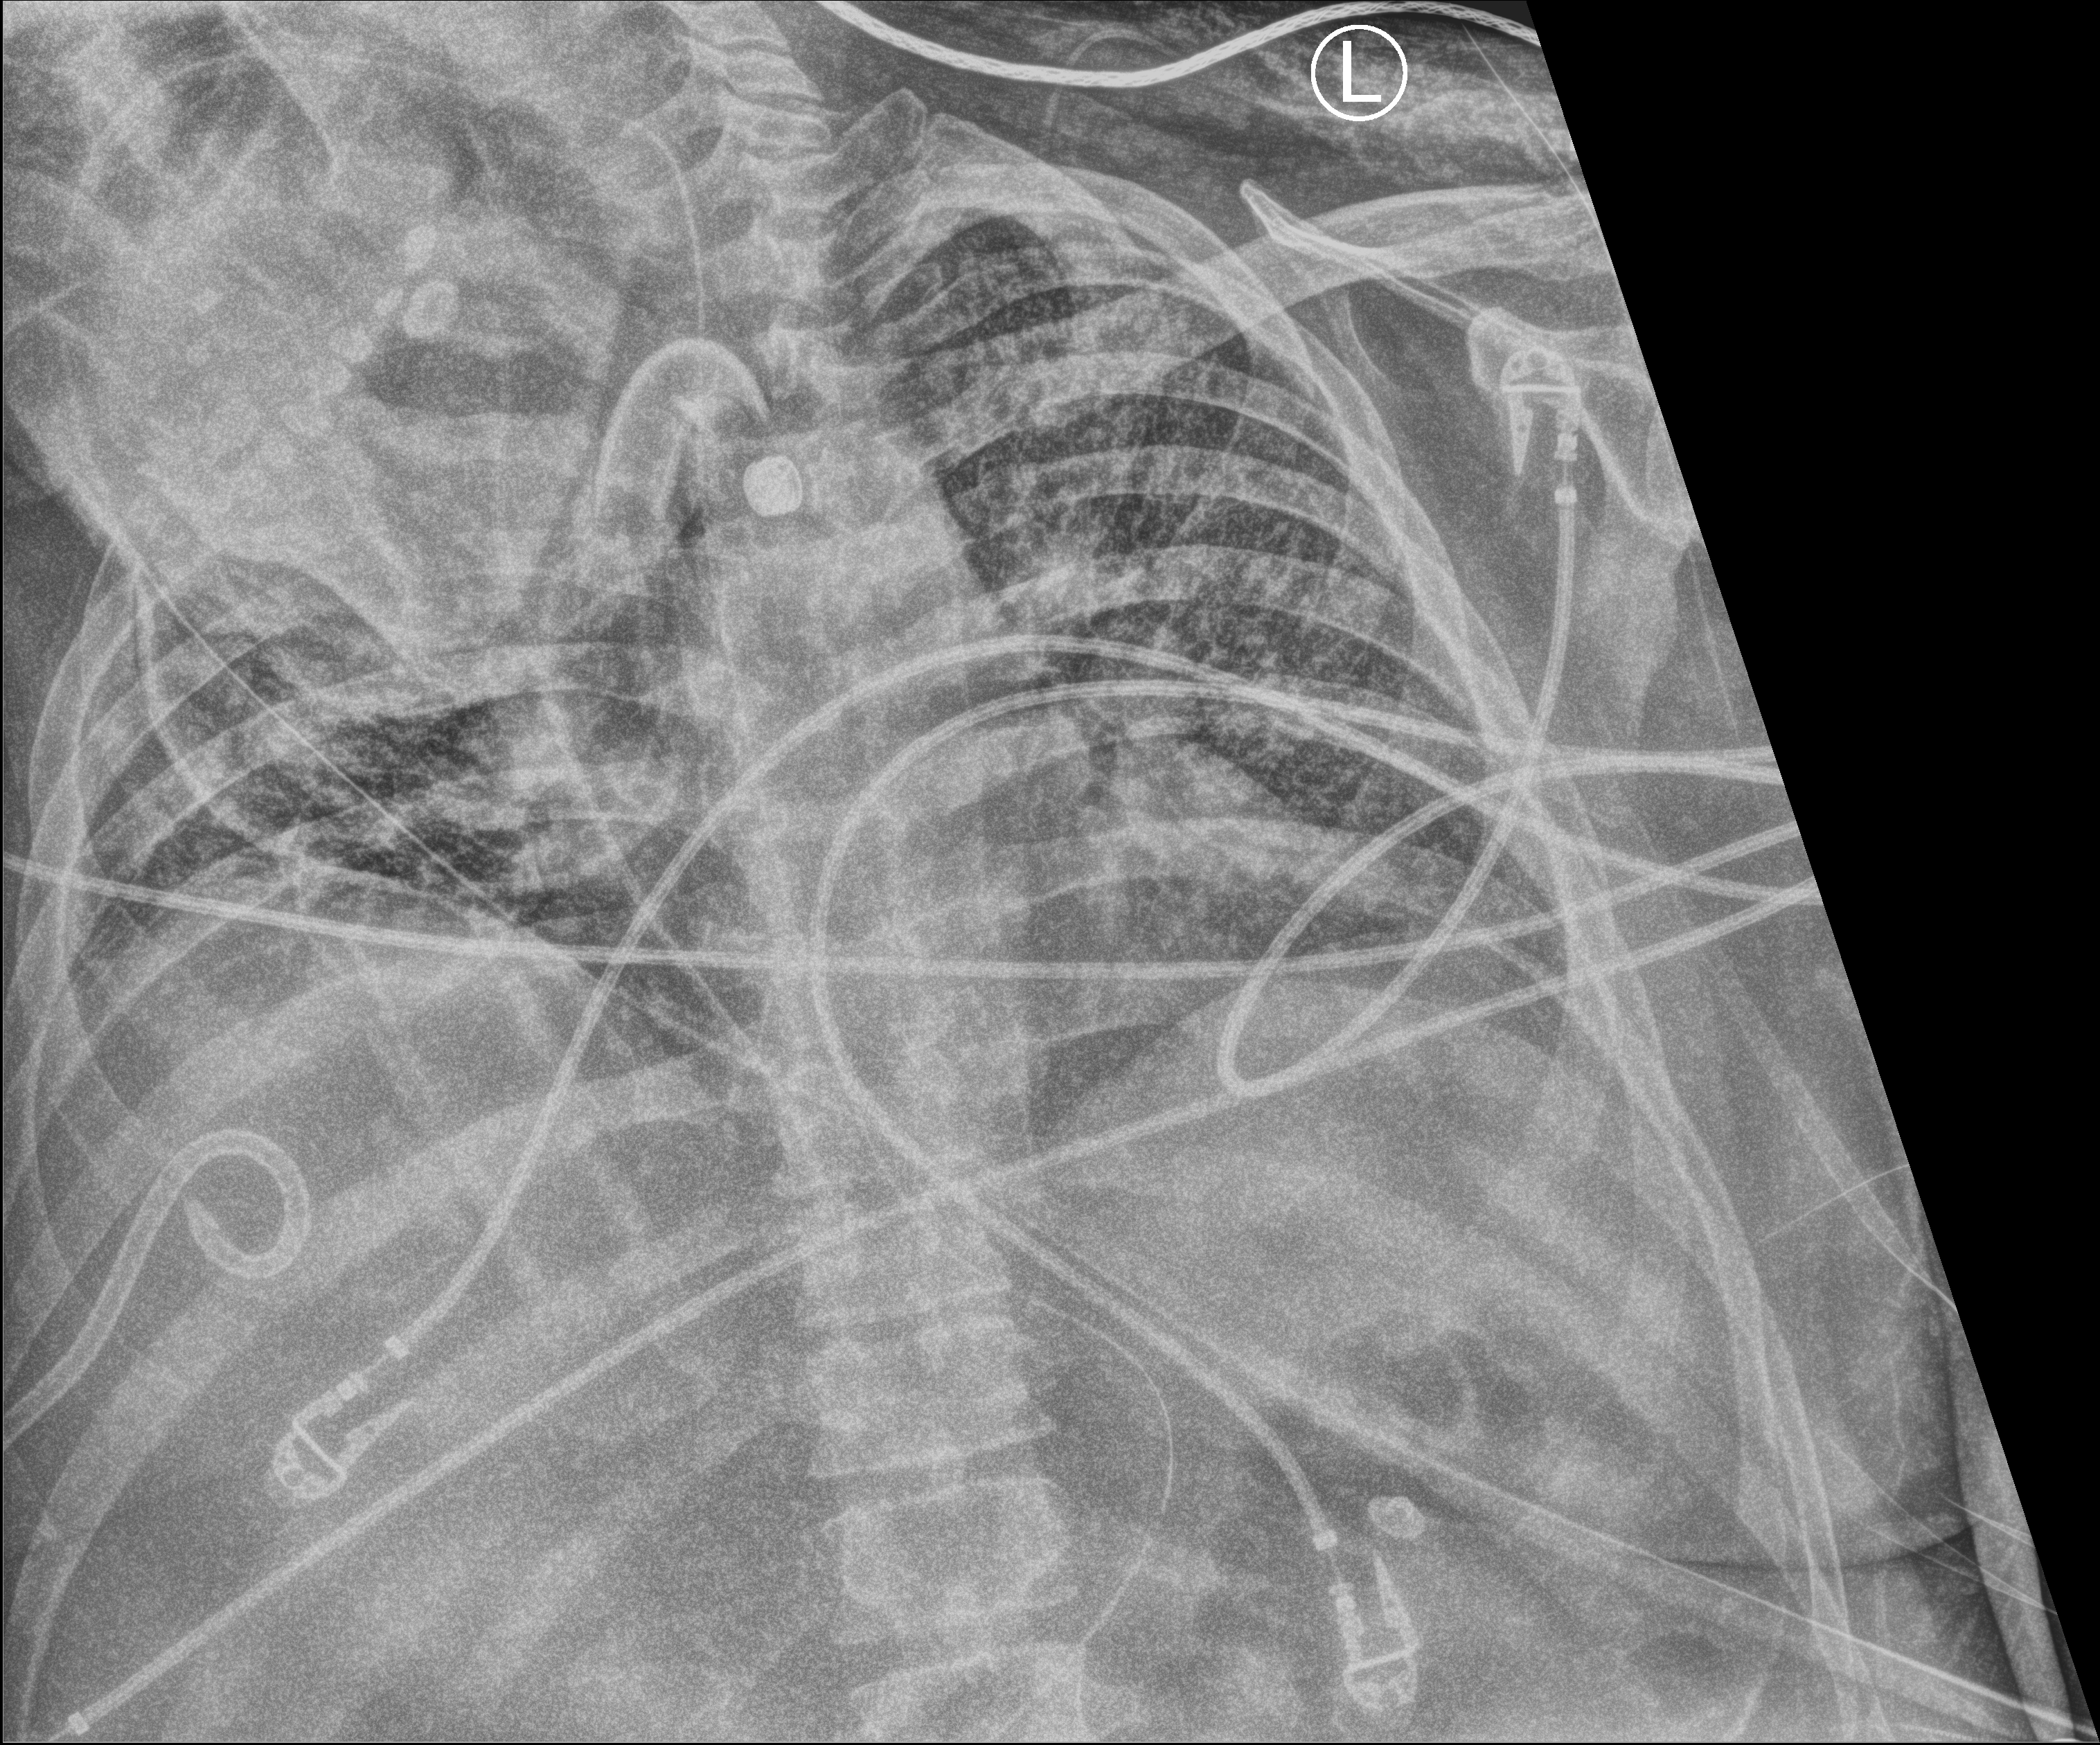
Portable chest radiograph; anteroposterior (AP) projection. Male patient hospitalised with COVID-19, age 18–59 years.
Admission-level facts for this patient (not findings on this image; timing relative to this image not recorded): admitted to intensive care during this hospital stay: yes; diabetes (admission record): no; length of hospital stay: 80 days.